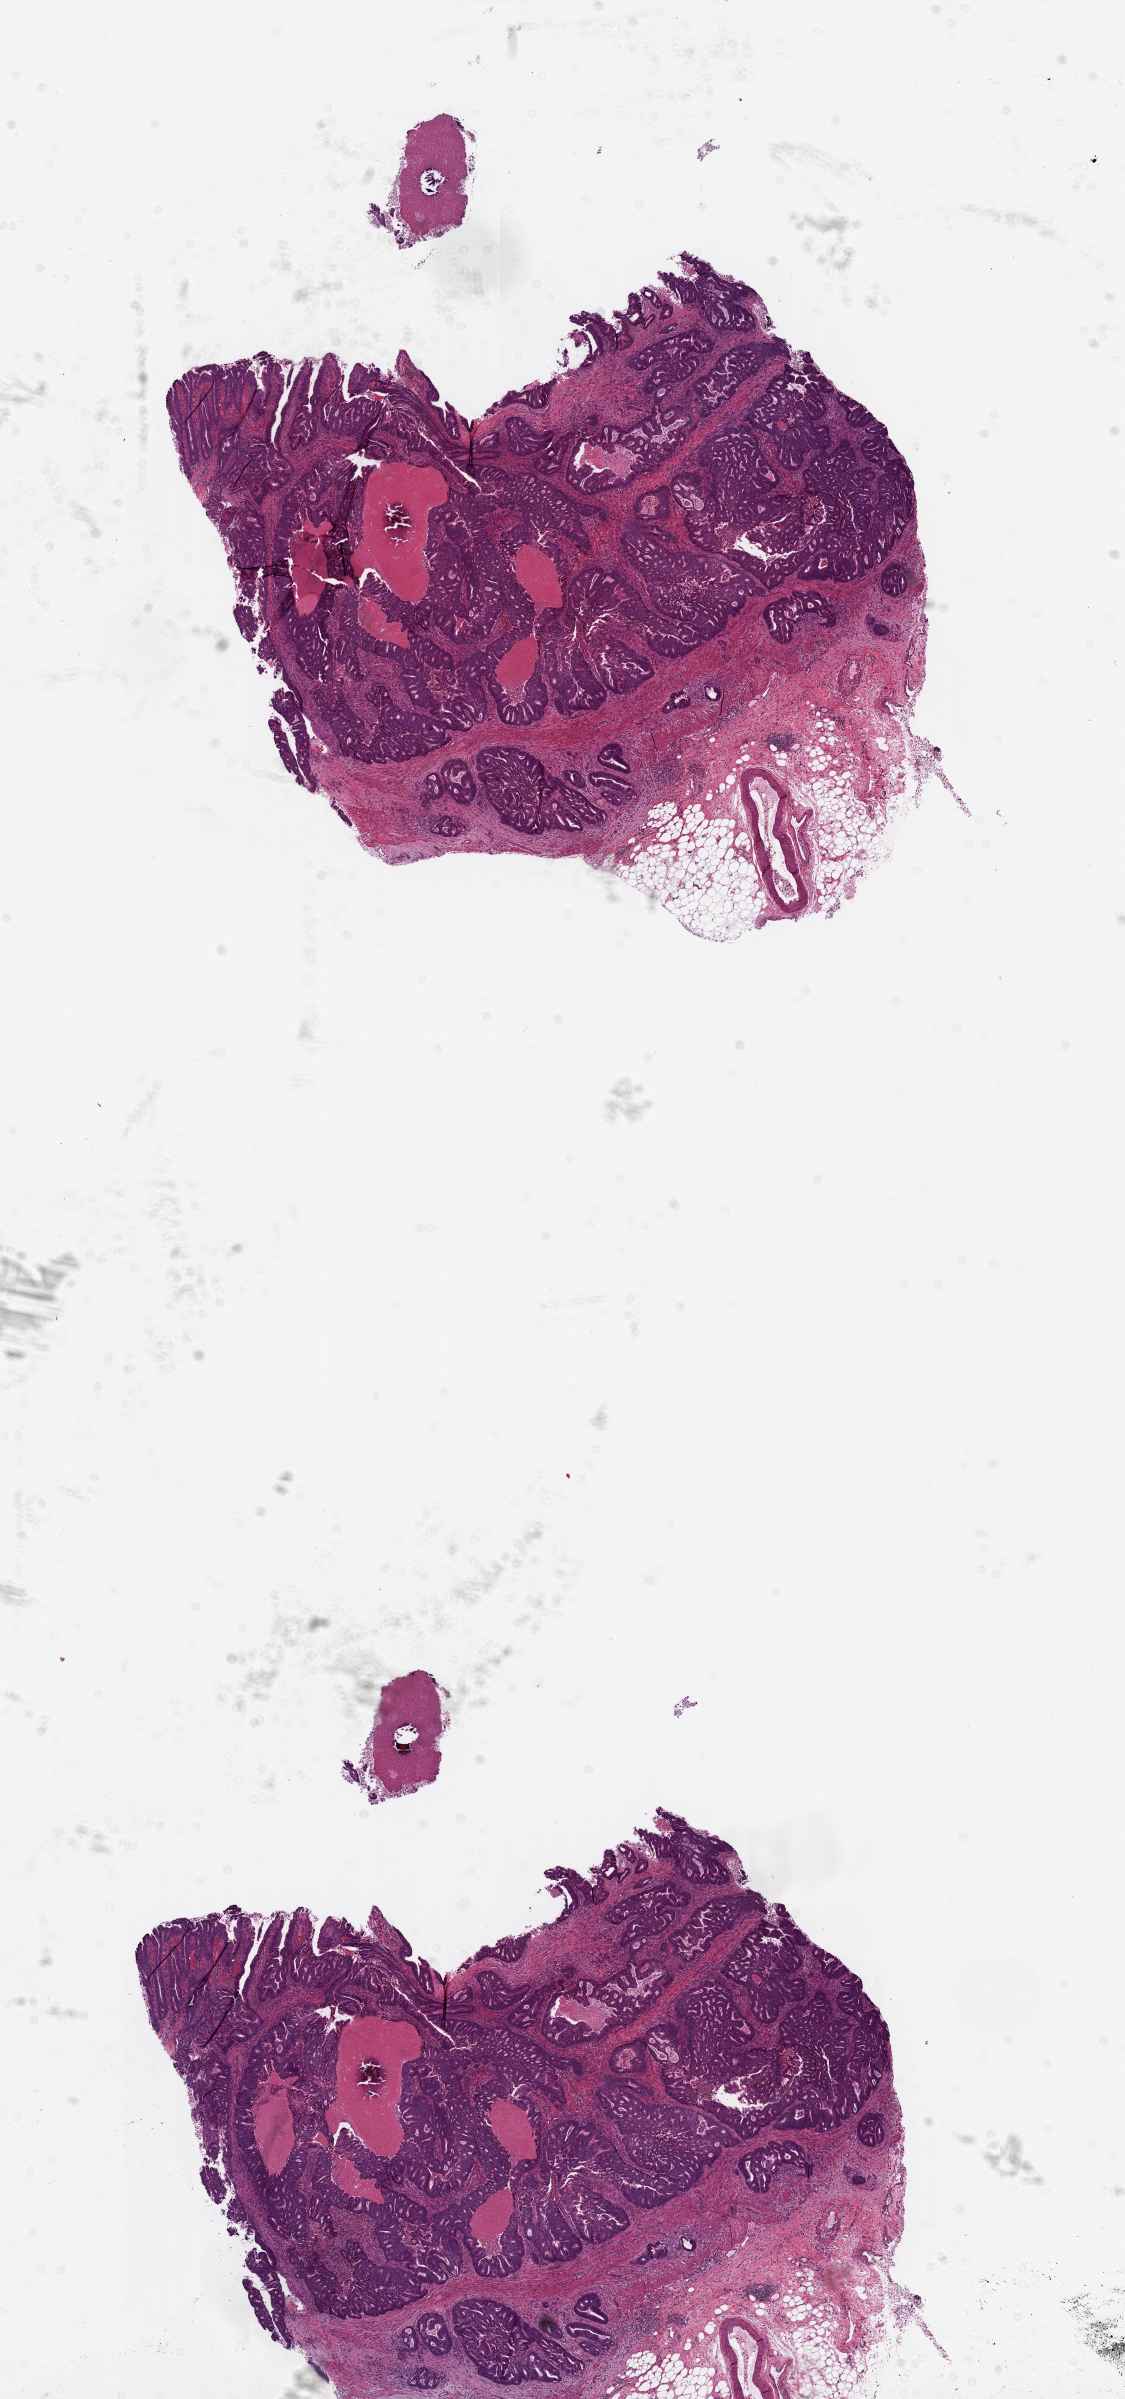
H&E-stained whole-slide image — shown as a low-resolution overview of the whole scanned area (about 9.0 x 19.2 mm, slide scanned at 20x); frozen section from the top of the tissue portion; sample: primary tumour, colon. Patient: female, age at initial diagnosis 68 years. Pathologist review of this section (percent, as recorded): tumour cells 73%, tumour nuclei 80%, normal cells 10%, stromal cells 5%, necrosis 12%.
AJCC pathologic stage: IIIC (6th edition). Pathologic diagnosis: Adenocarcinoma, NOS (ascending colon).